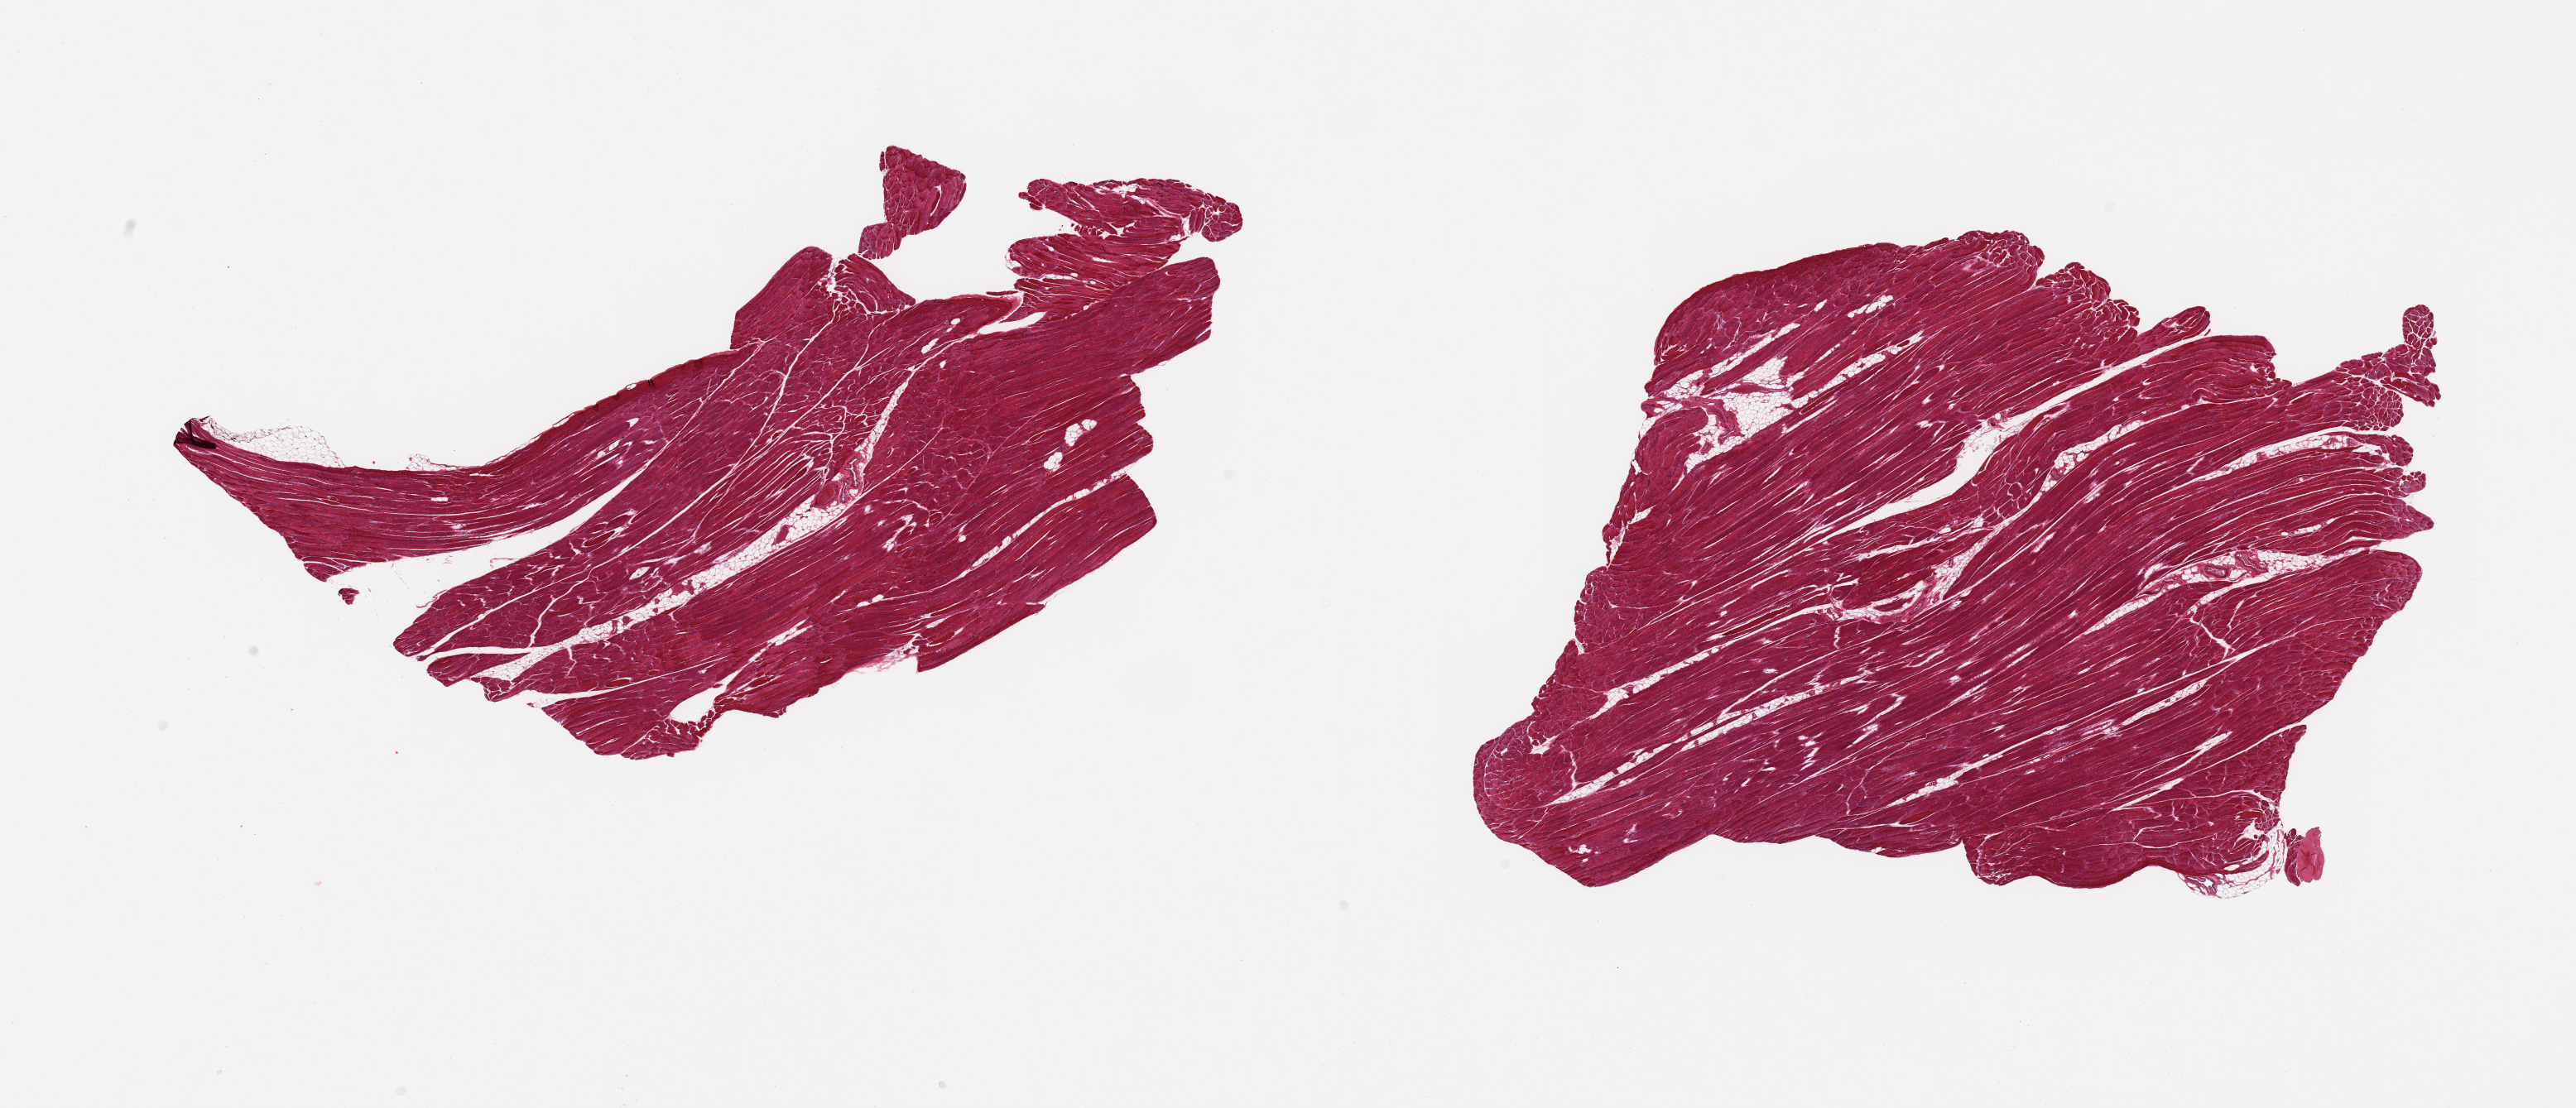
Whole-slide image, haematoxylin and eosin stain — whole scanned area (about 24.6 x 10.6 mm) shown as a low-resolution overview; PAXgene-fixed, paraffin-embedded tissue; sampled site (target tissue): skeletal muscle; tissue donor sample. Donor sex: female.
Reviewer comment on this tissue sample: 2 pieces; 5% internal fat.